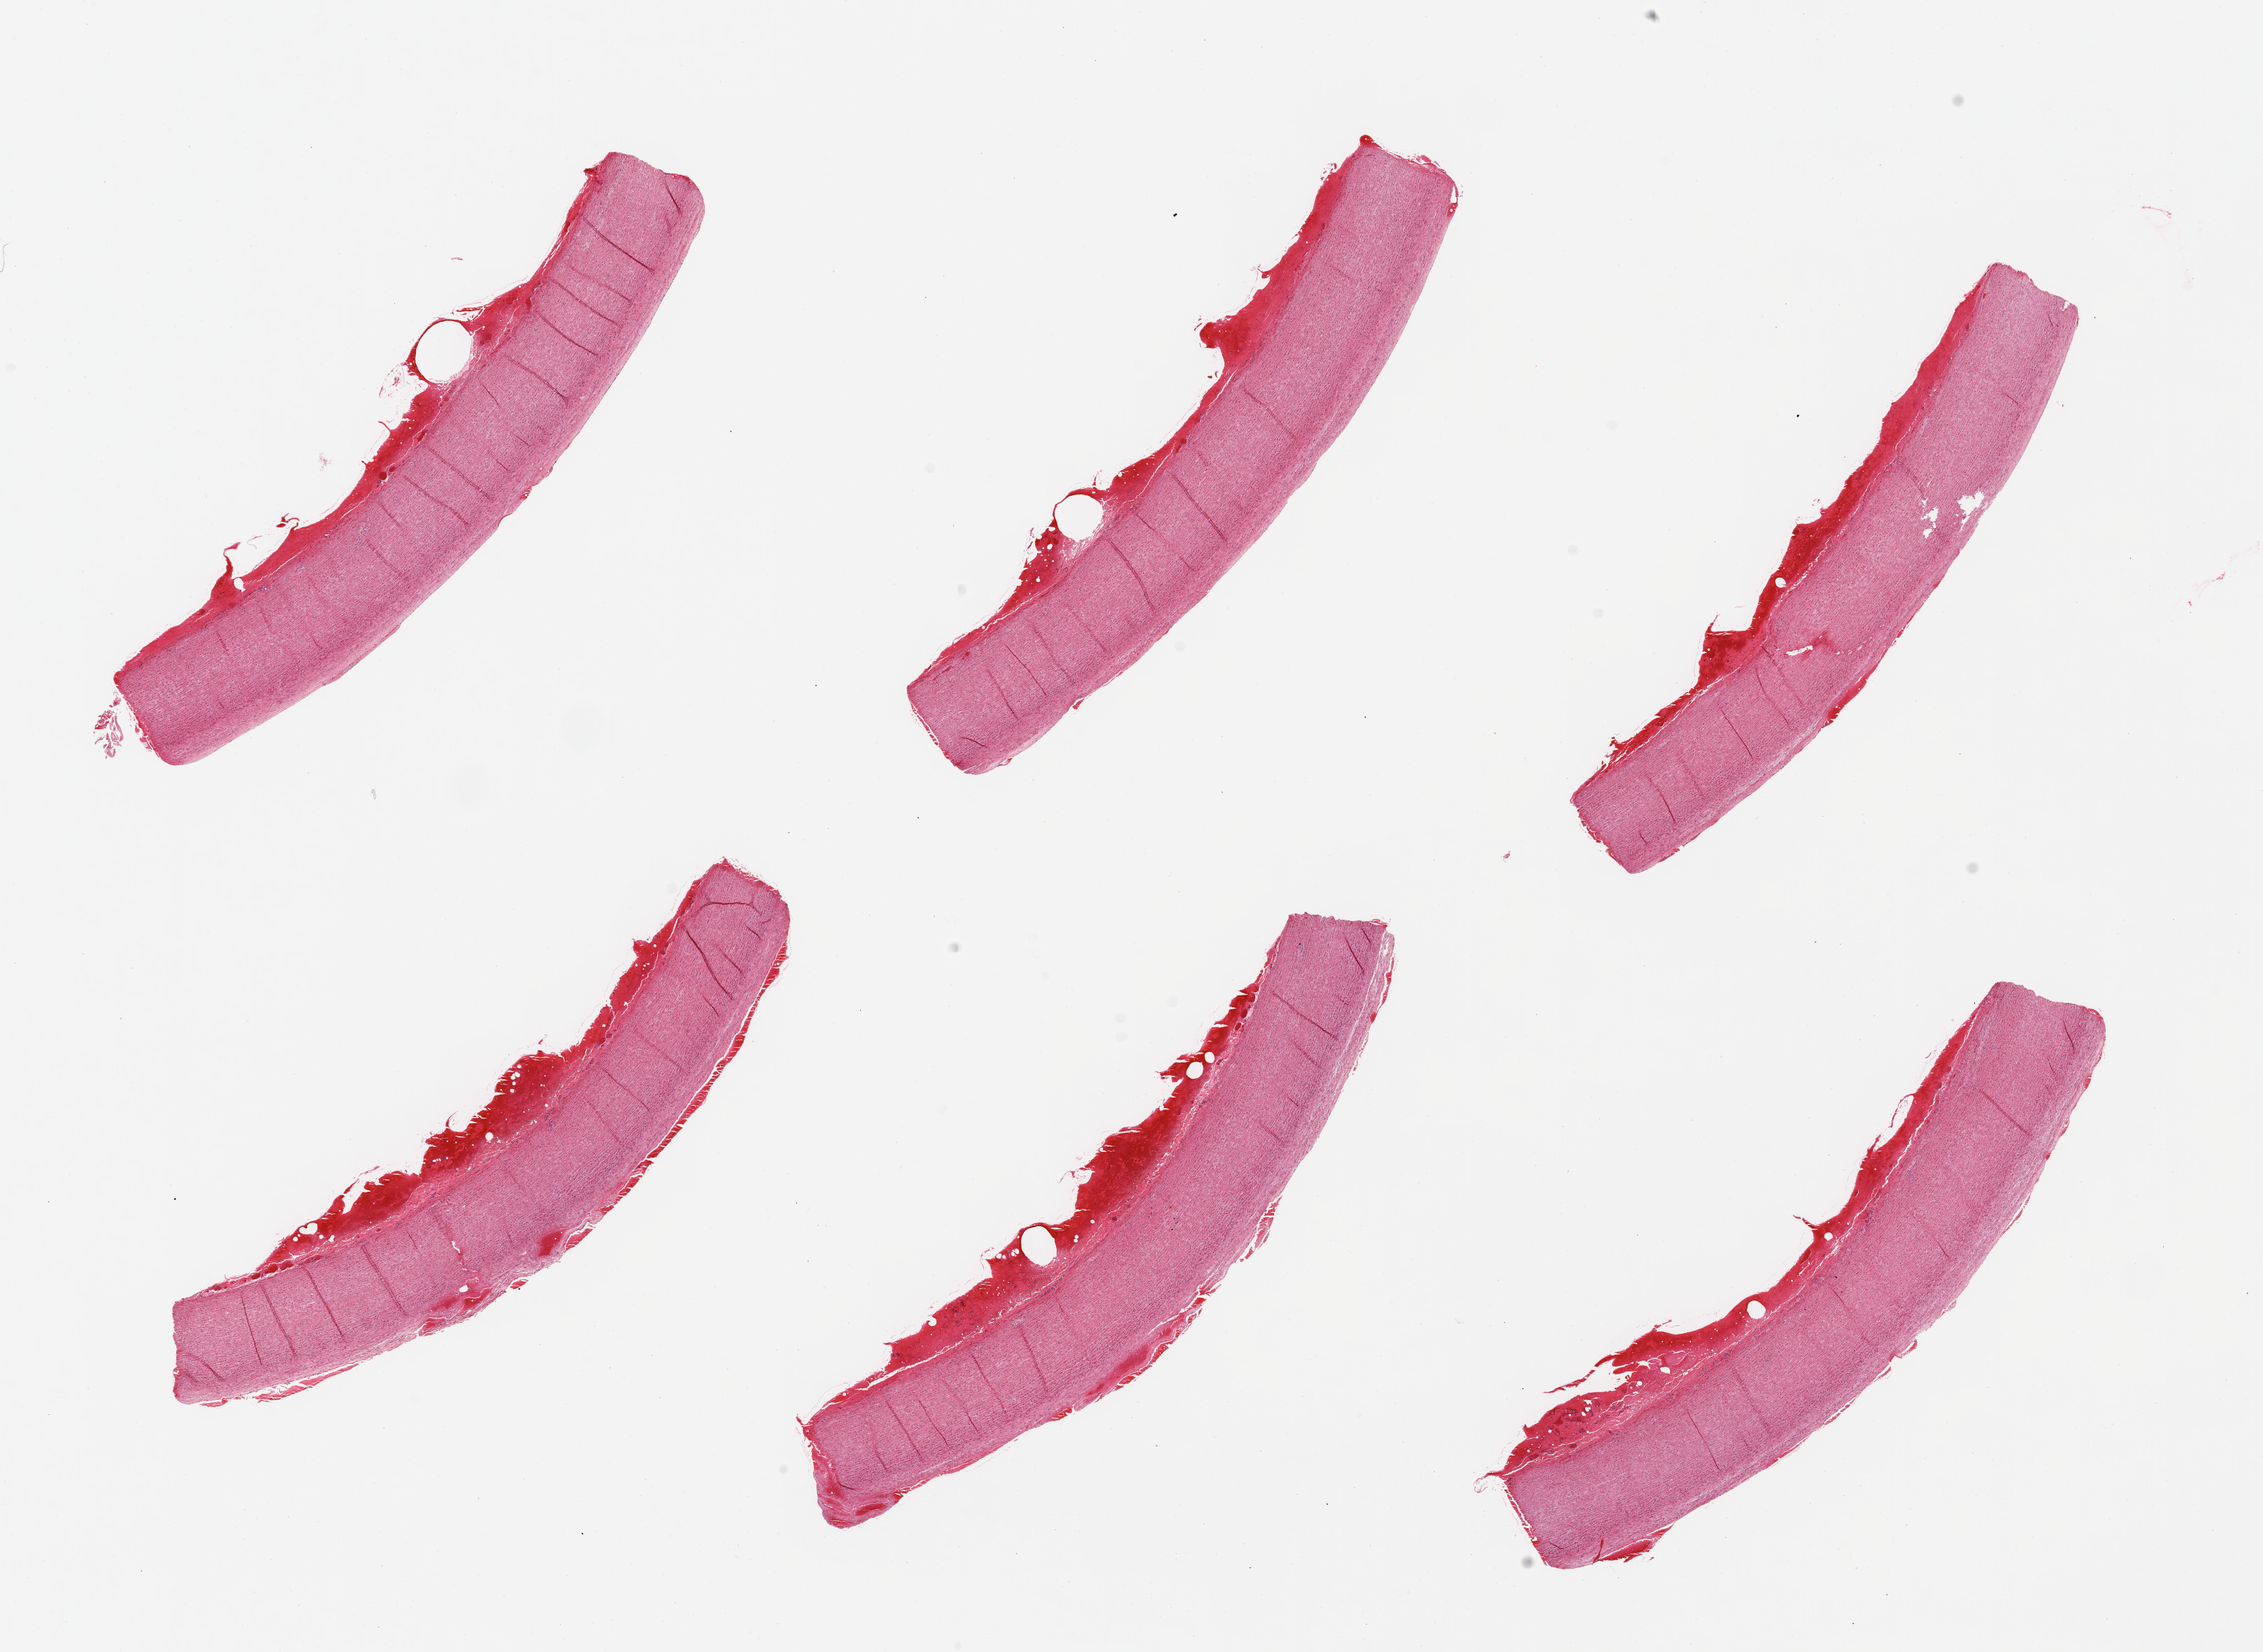
Digitized haematoxylin and eosin-stained section, a low-resolution overview of the entire scanned area, about 25.6 x 18.7 mm. PAXgene-fixed, paraffin-embedded tissue. Sampled site (target tissue): aorta. Donor tissue sample.
Pathologist's review note for this sample: 6 pieces; no plaques; external blood coating up to 0.5mm thick.